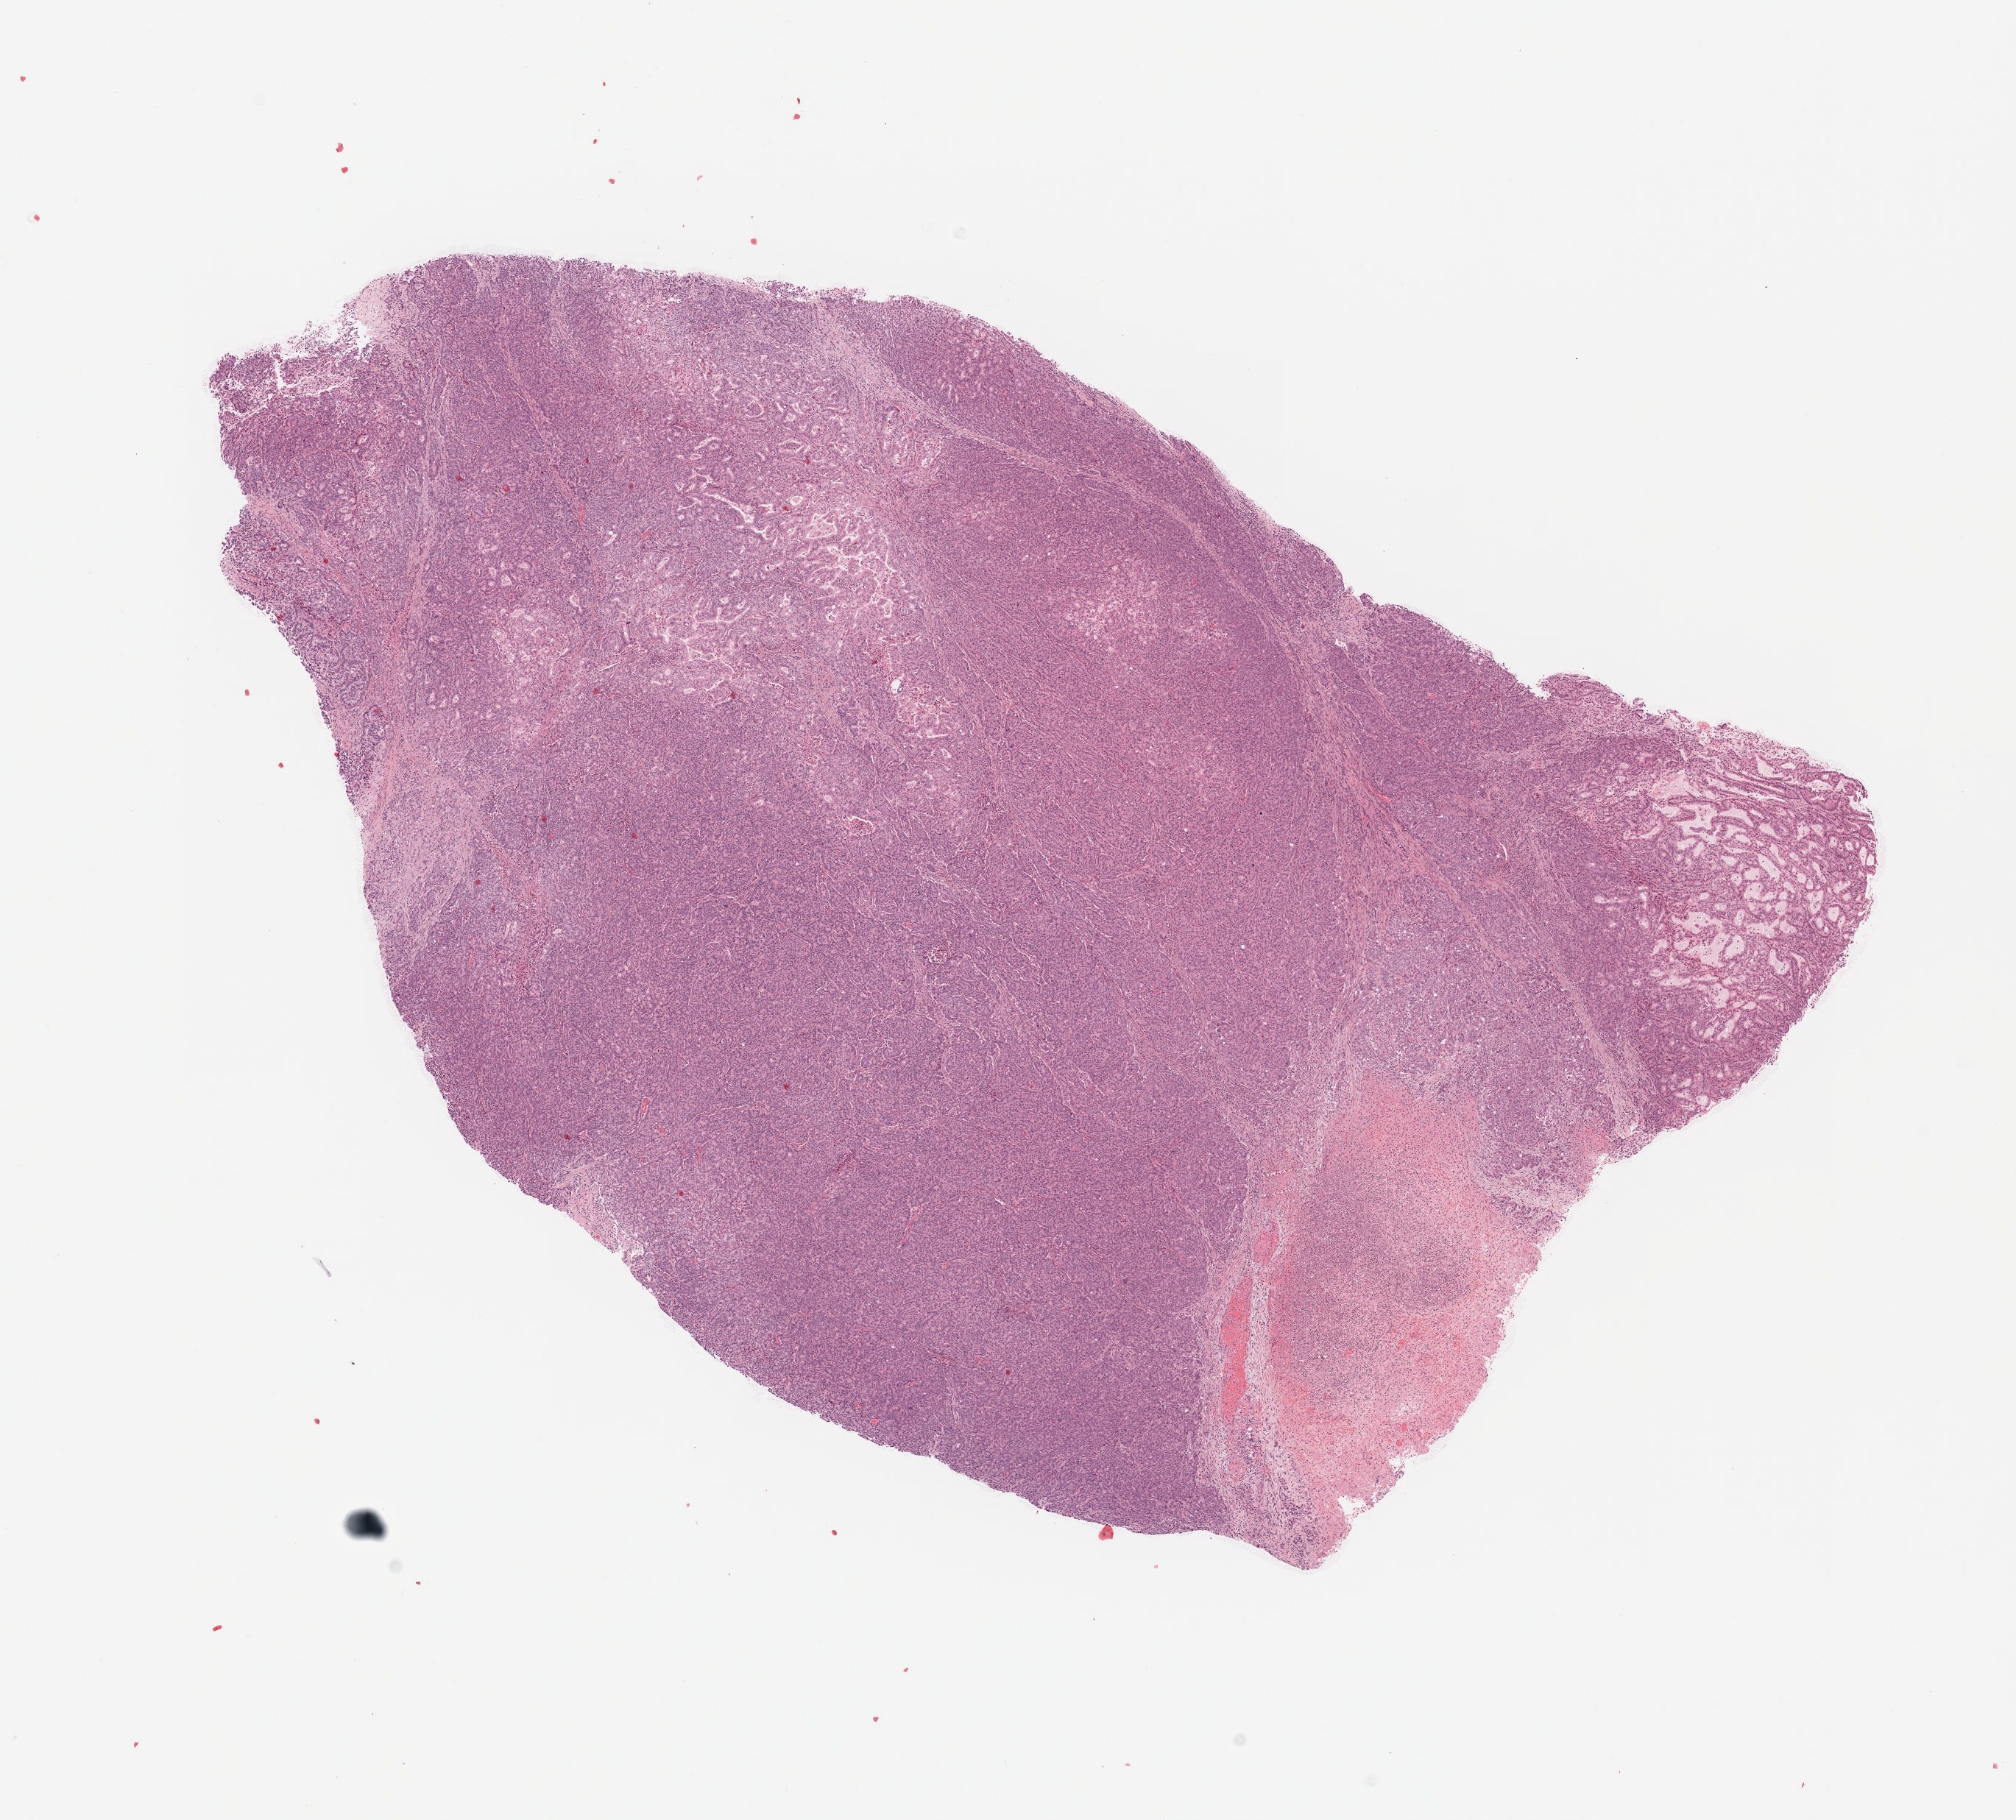
Whole-slide histology image, H&E-stained, low-resolution overview of the scanned area, about 10.9 x 9.8 mm (from a 20x scan), formalin-fixed paraffin-embedded (FFPE) diagnostic section, sample: primary tumour, stomach. Male patient; age at initial diagnosis 78 years. Histologic grade: G3 (poorly differentiated).
Lymph nodes positive (case pathology): 1 of 35 examined. AJCC pathologic stage: II (6th edition). Pathologic diagnosis: Carcinoma, diffuse type (cardia, NOS).